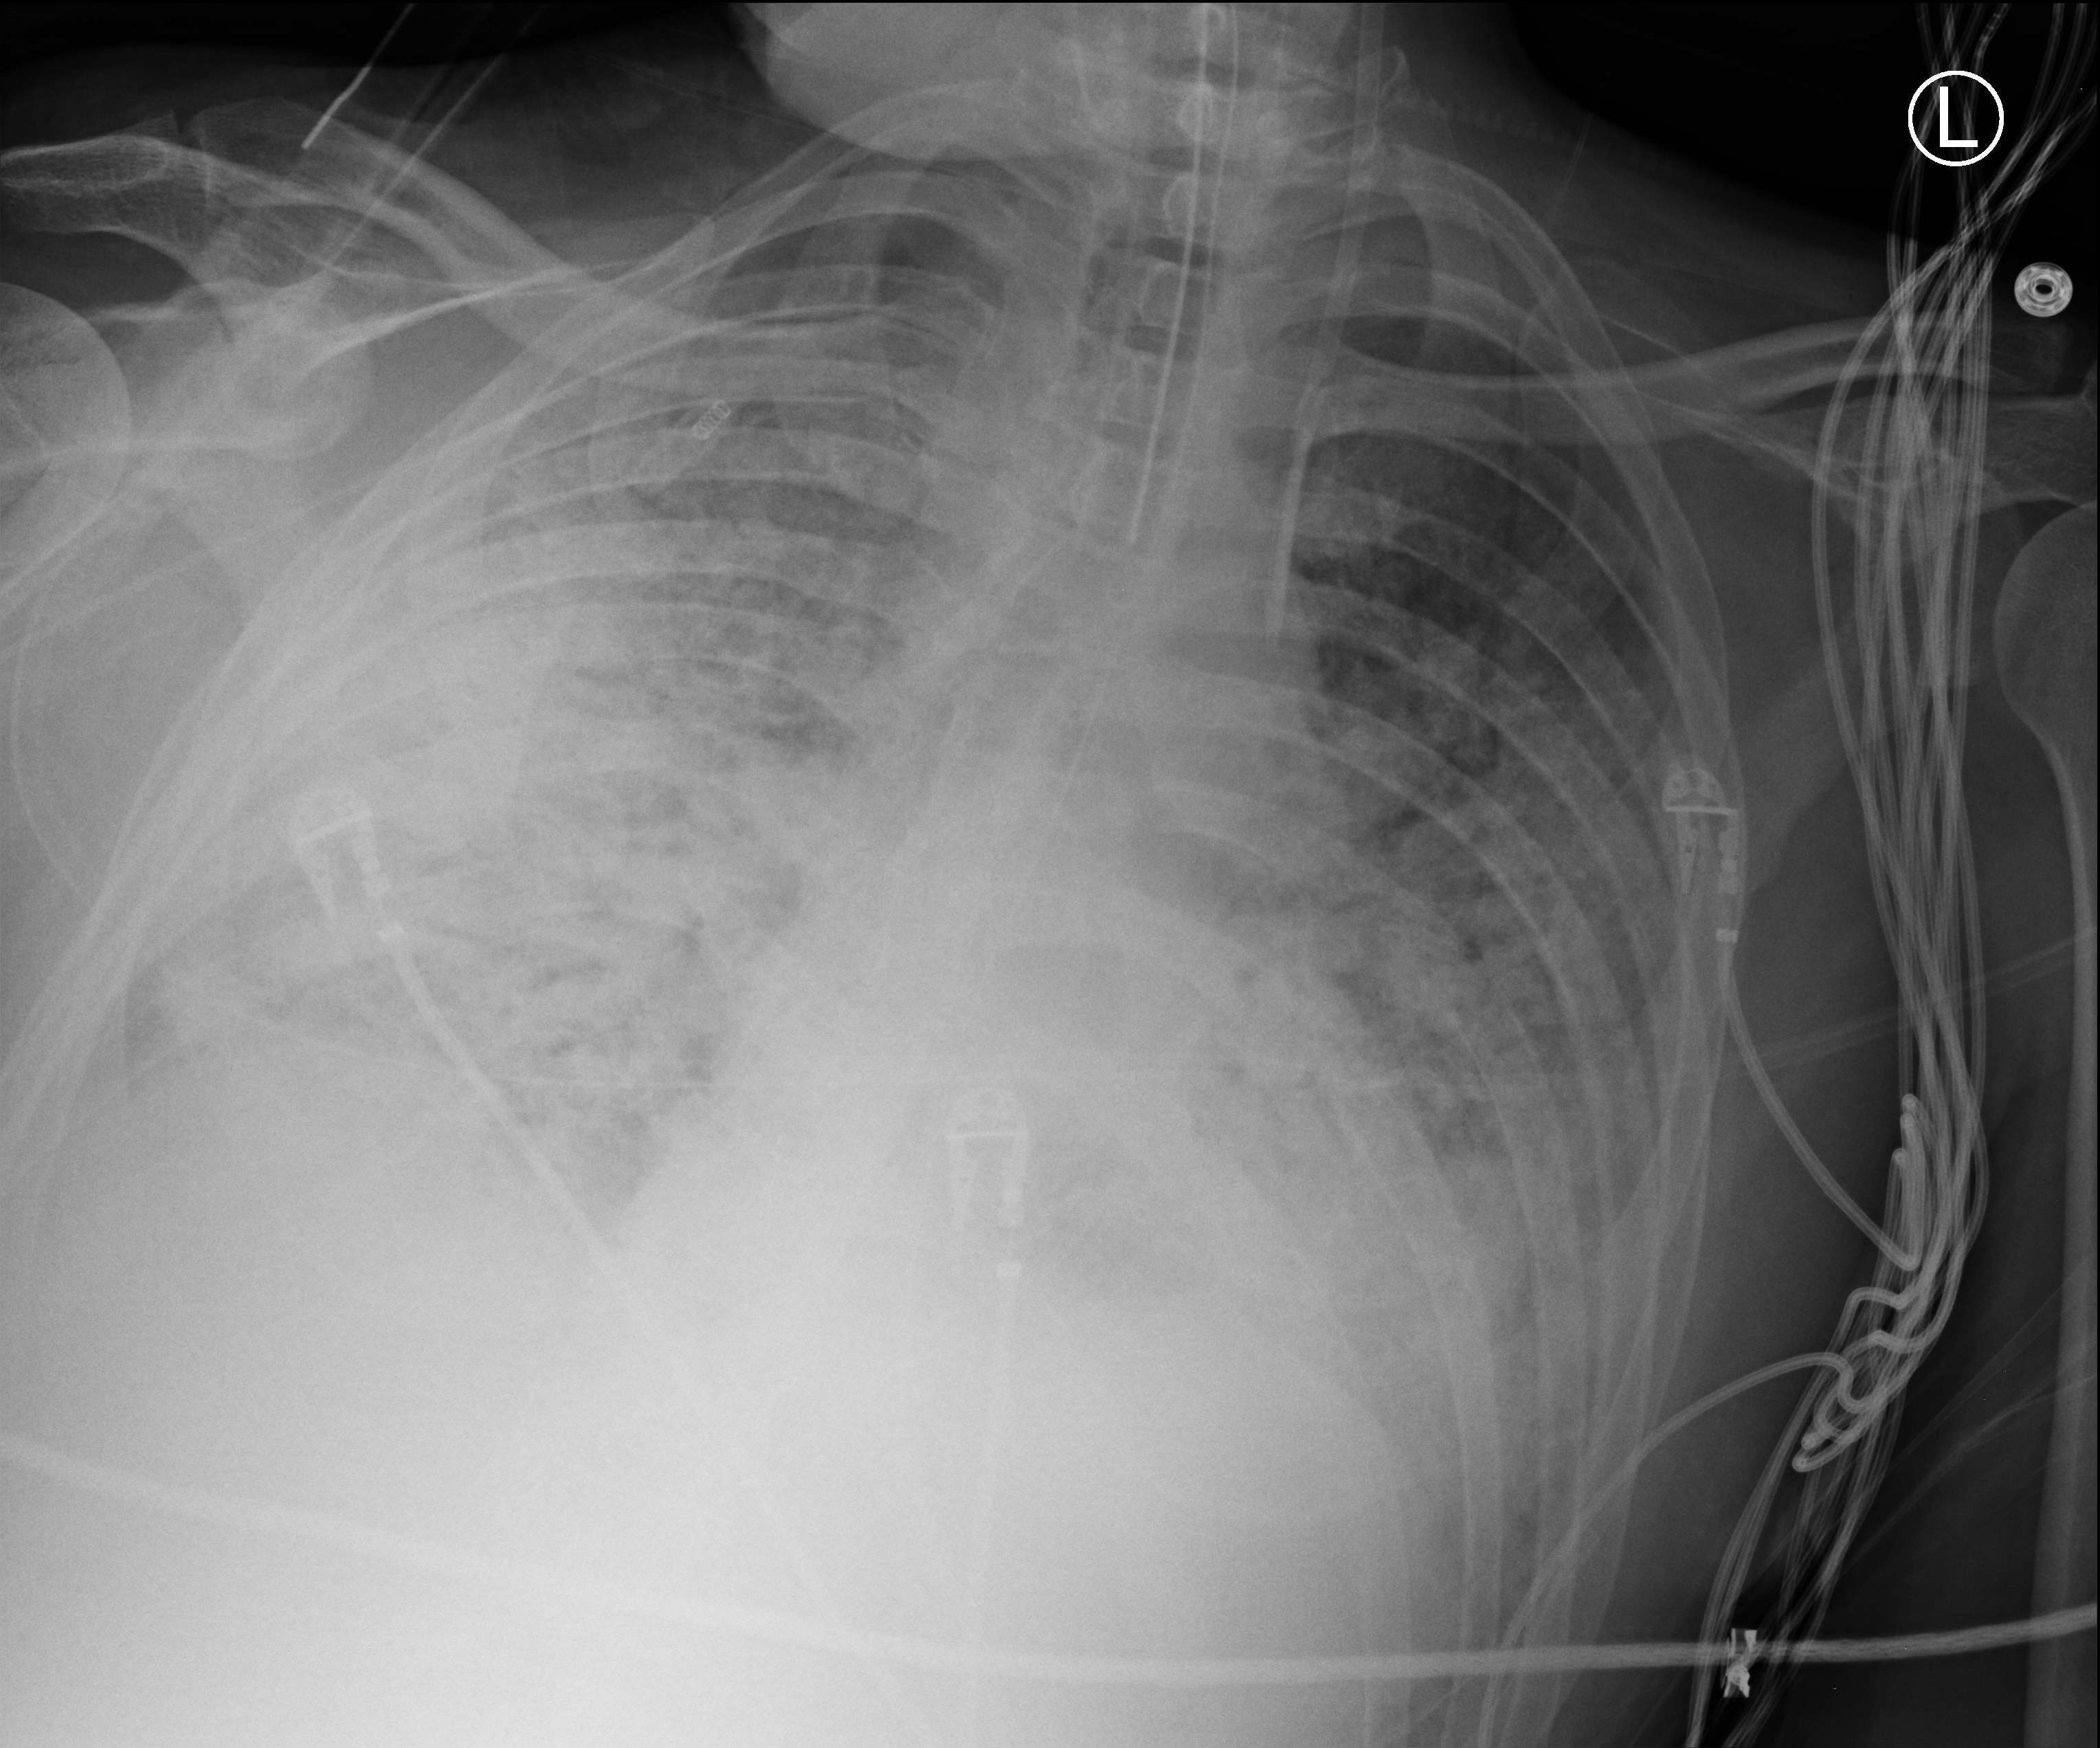
Portable chest radiograph; anteroposterior (AP) projection. Patient hospitalised with COVID-19; male, aged 18–59 years.
Hospital-stay facts (about this admission, not read from this image; timing relative to this image not recorded):
- length of hospital stay: 75 days